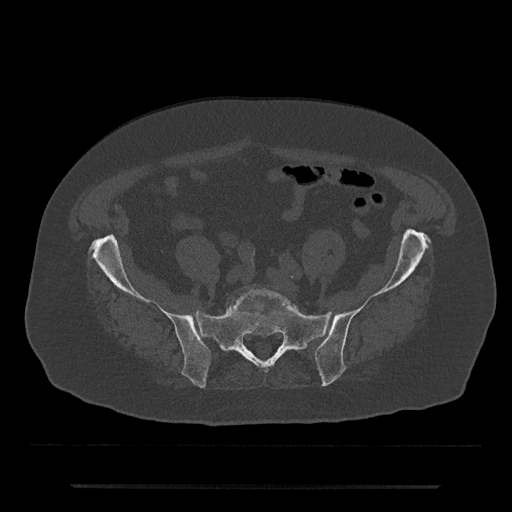
CT including the spine, one axial slice. Position 240 of 797 along the scan axis. Reconstruction kernel Br40s/3. 120 kVp. Bone window (W 1800 / L 400 HU). 0.5 mm slice thickness. 512 × 512 image matrix, field of view 434 × 434 mm. Male patient, age 80 years. Case-level facts recorded for this patient, not image findings: primary cancer: prostate; vertebrae with lytic lesions (as recorded): L1, T11.
Structures marked on this image (semi-automatically segmented with operator editing):
- L5 vertebra: bounding box (x1, y1, x2, y2) in pixels: (231, 289, 299, 312)